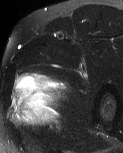
MRI of an extremity soft-tissue mass, one axial slice; T2-weighted fat-saturated; MR volume resampled by the dataset authors to the PET/CT grid (not the native acquisition matrix); 123 × 153 image matrix. Male patient. Case-level facts recorded for this patient, not image findings: histological type: pleiomorphic liposarcoma; grade: high; site of the primary tumour: left thigh.
Outlined on this slice (expert contour drawn on MRI and transferred to this co-registered scan by the dataset authors):
- gross tumour volume including surrounding oedema: box from (x=11, y=72) to (x=69, y=130) px
- gross tumour volume (mass): (x=20, y=77)–(x=57, y=107)